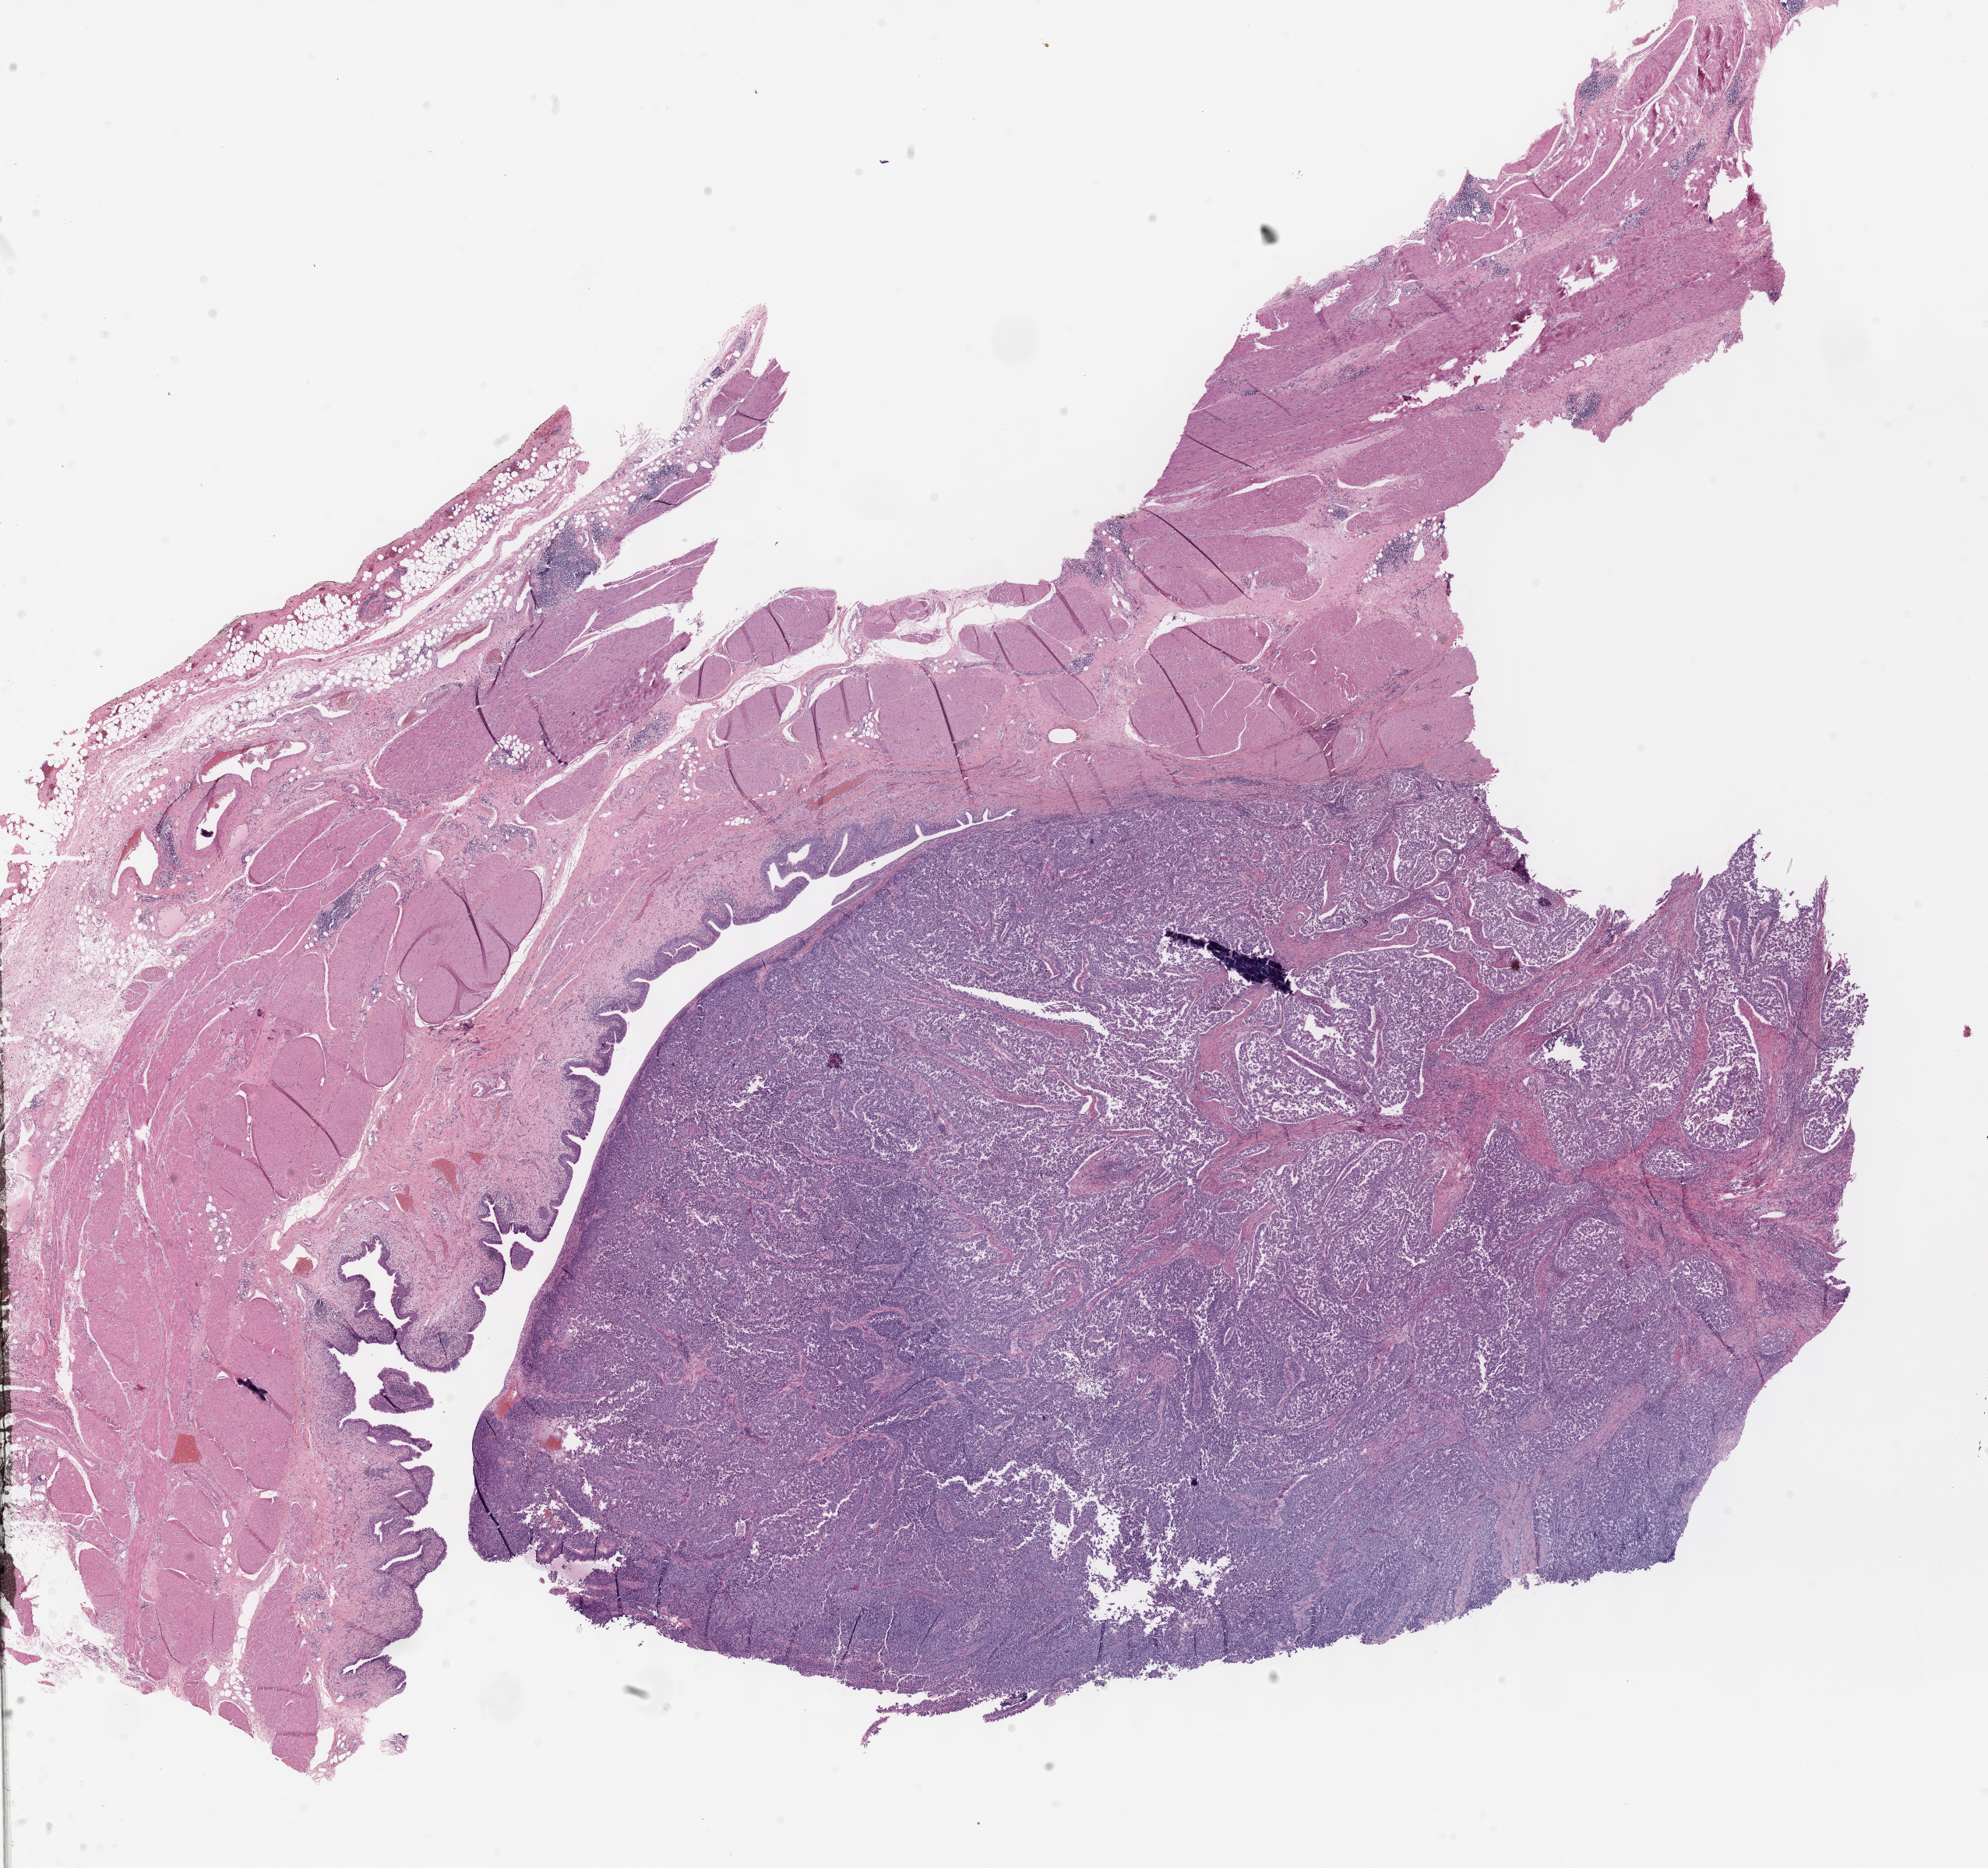
H&E whole-slide image, whole scanned area (about 20.6 x 19.4 mm, from a 40x scan) shown as a low-resolution overview, FFPE section, bladder, primary tumour sample. Patient: male, age at initial diagnosis 73 years.
Pathologic diagnosis: Papillary transitional cell carcinoma (trigone of bladder).